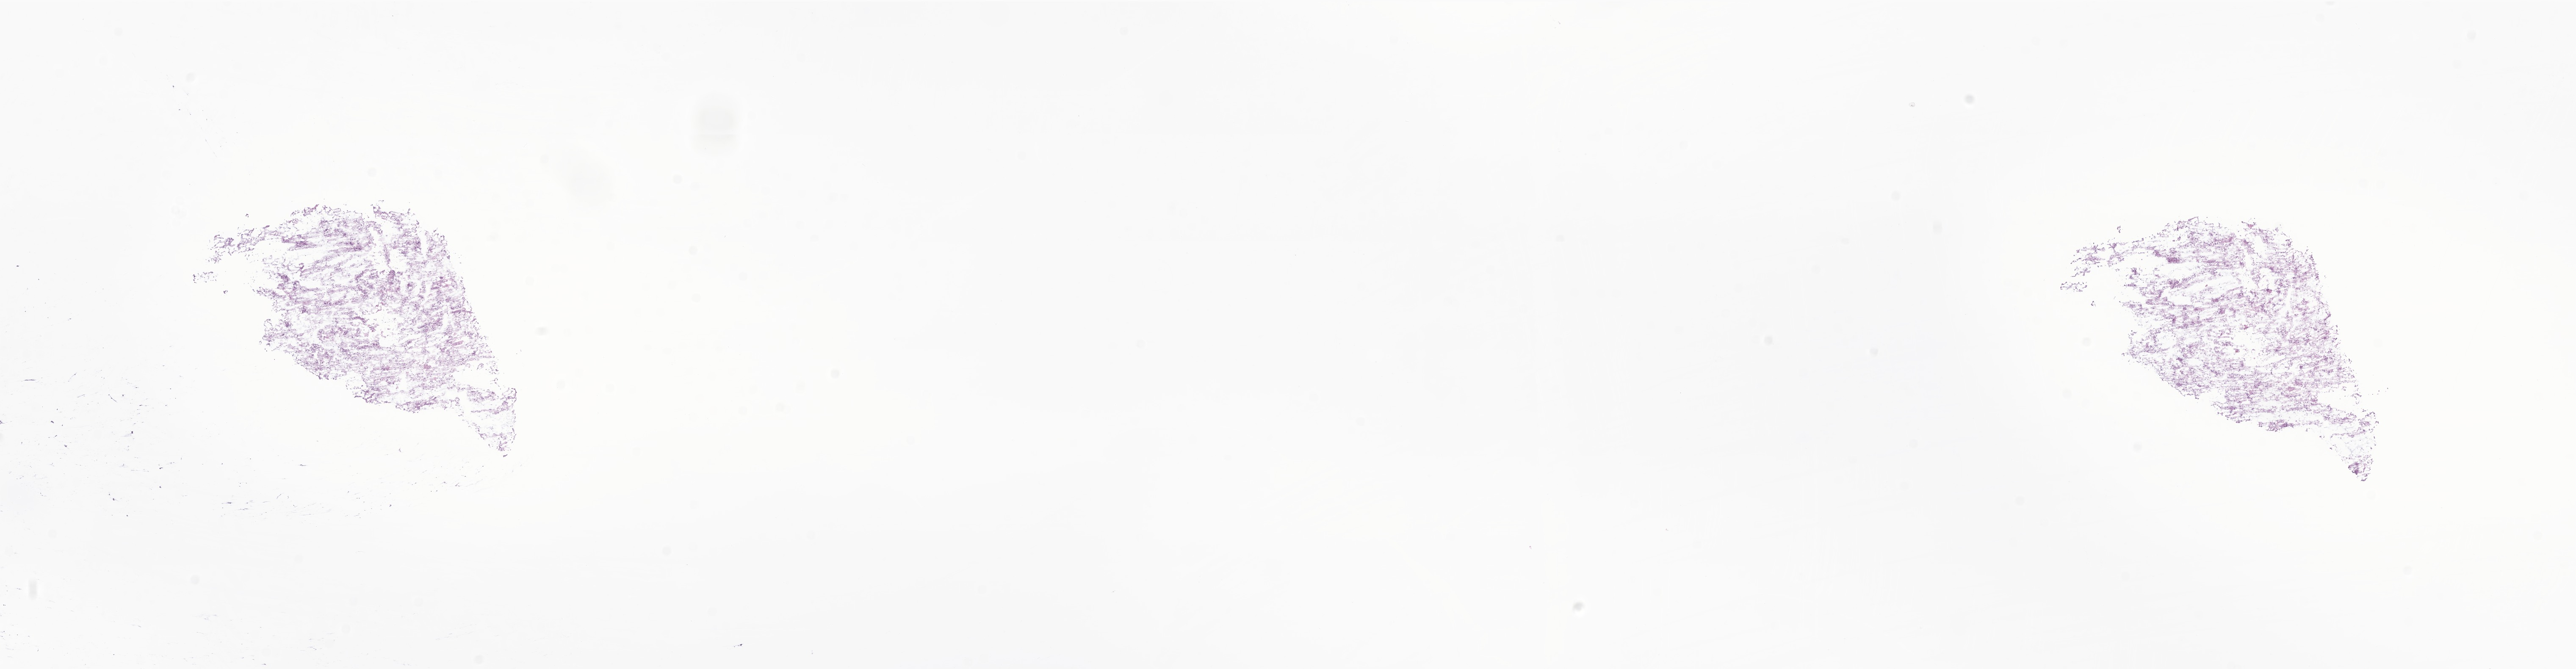
Whole-slide image, H&E stain of tumor tissue from the brain, a low-resolution overview of the entire scanned area, about 25.6 x 6.7 mm. Cryosection (OCT / tissue freezing medium). Patient male; age 164 months (13 years 8 months).
- recorded diagnosis: Pilocytic astrocytoma